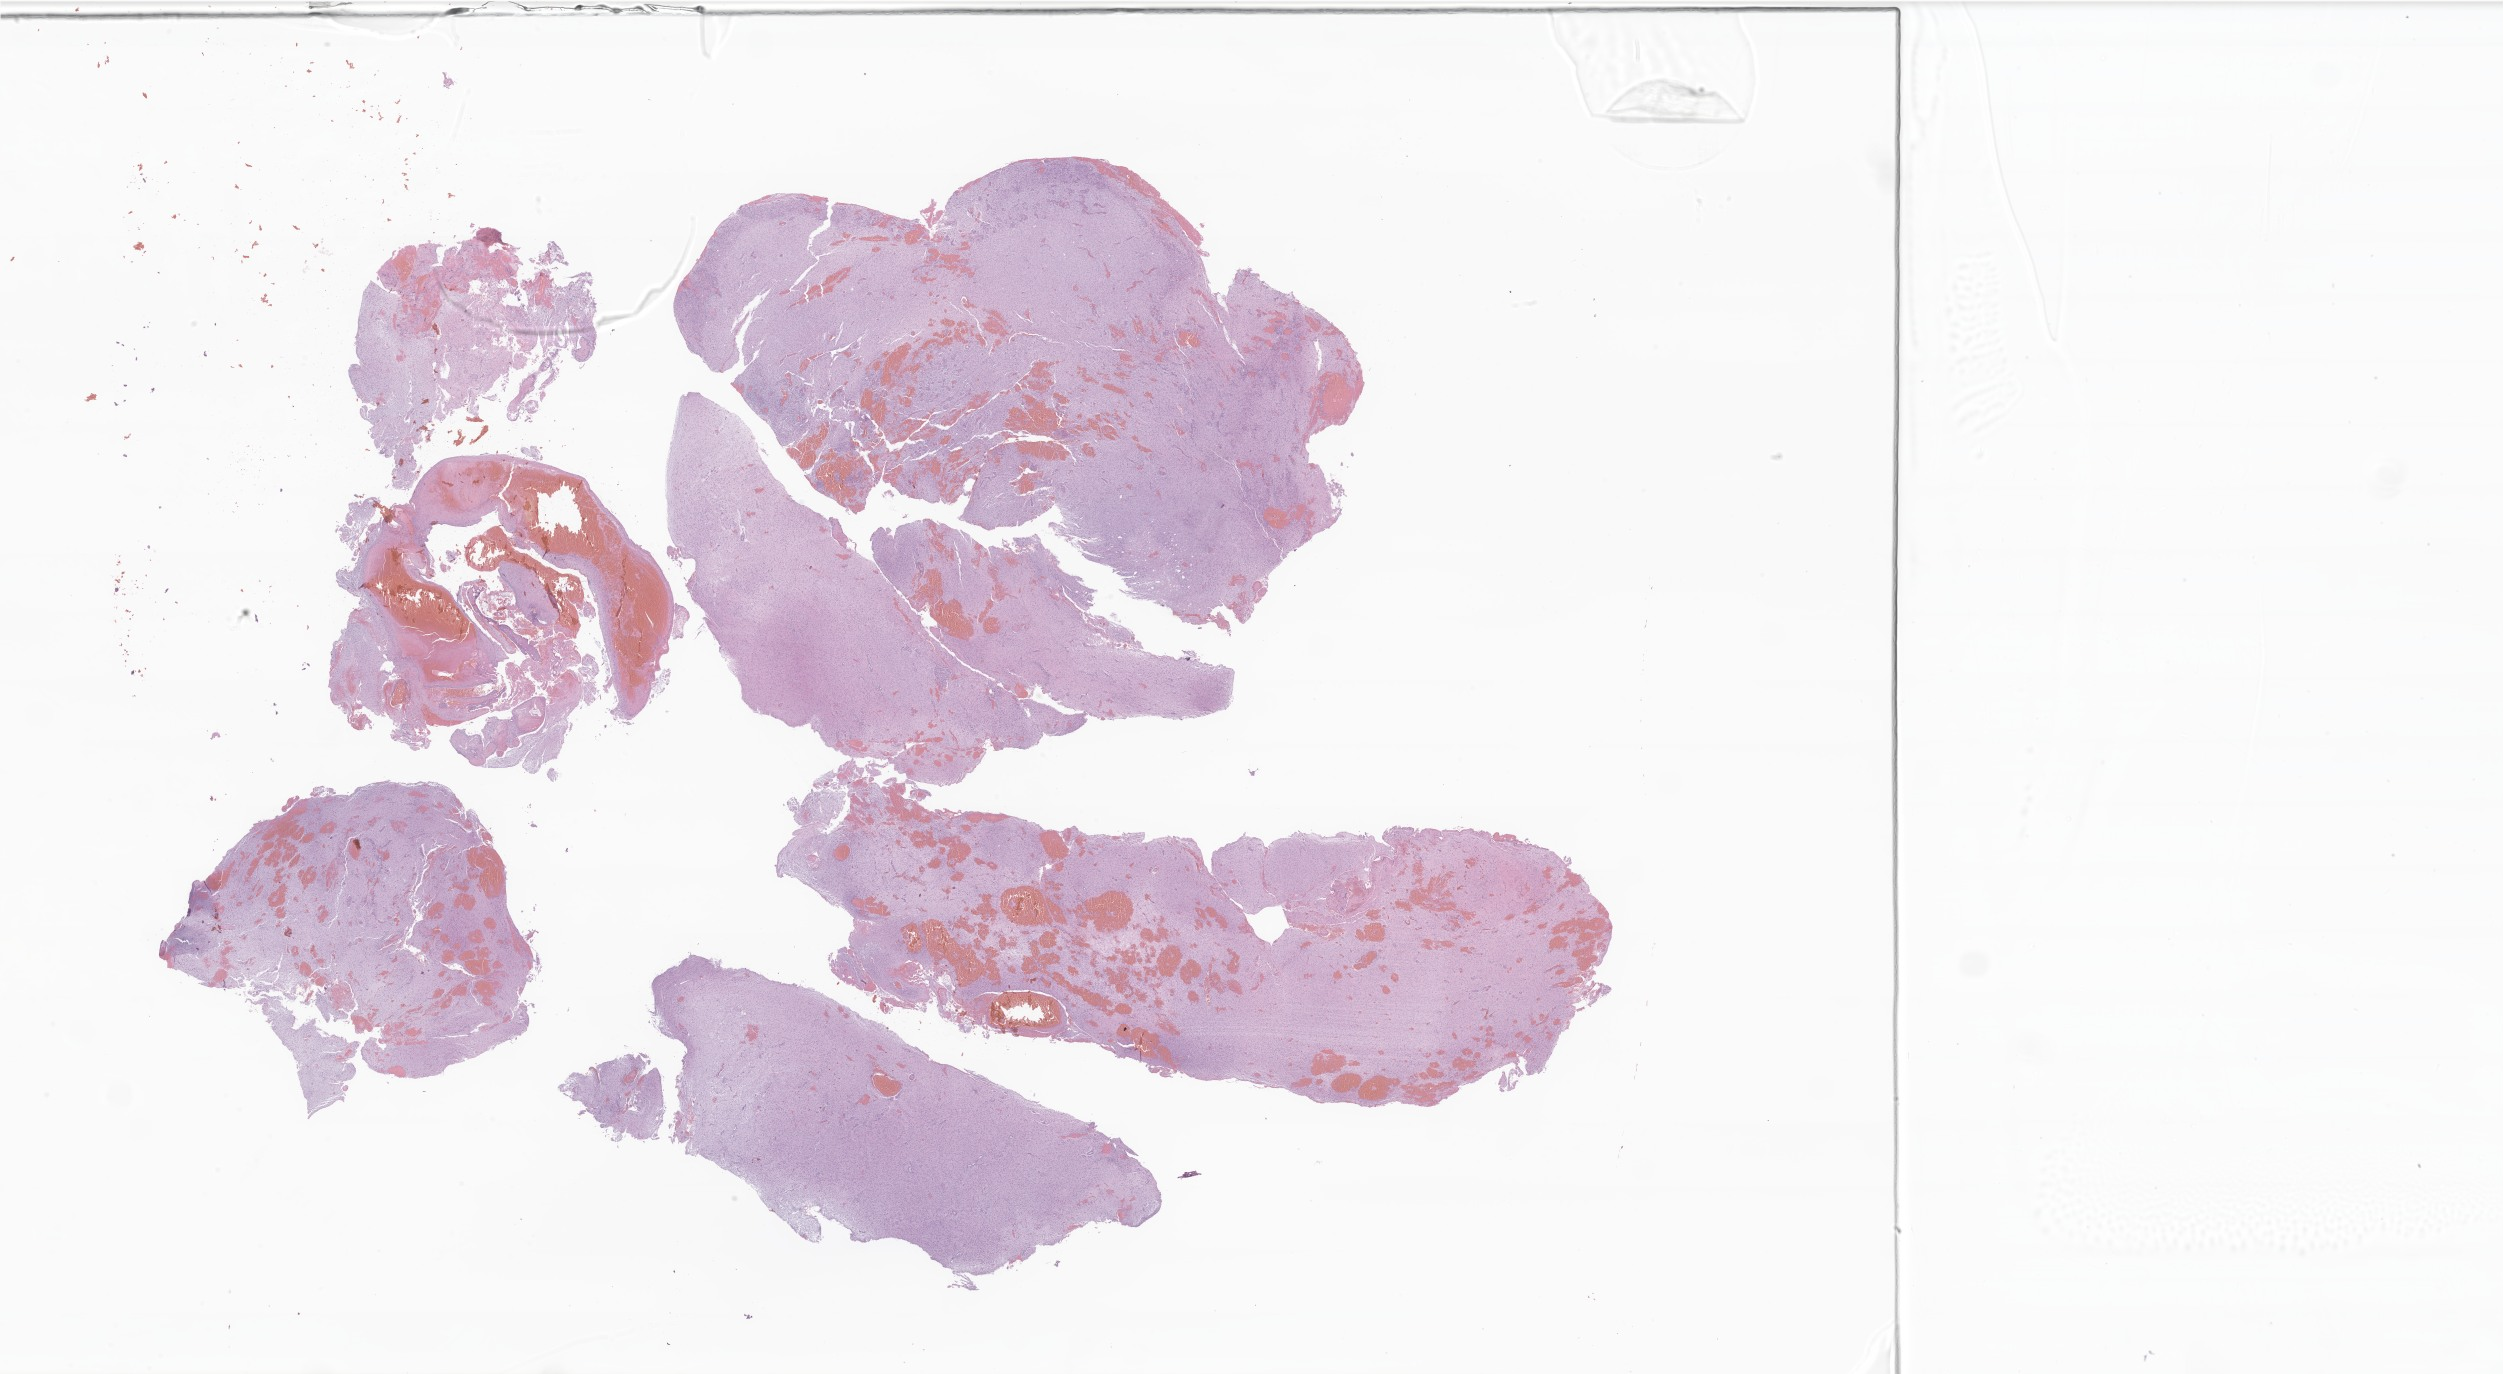
Digitized haematoxylin and eosin-stained section of tumor tissue from the brain — a low-resolution overview of the entire scanned area, about 42.2 x 23.2 mm. Formalin-fixed paraffin-embedded section. Male patient, age 120 months (10 years).
• recorded diagnosis: Pilocytic astrocytoma